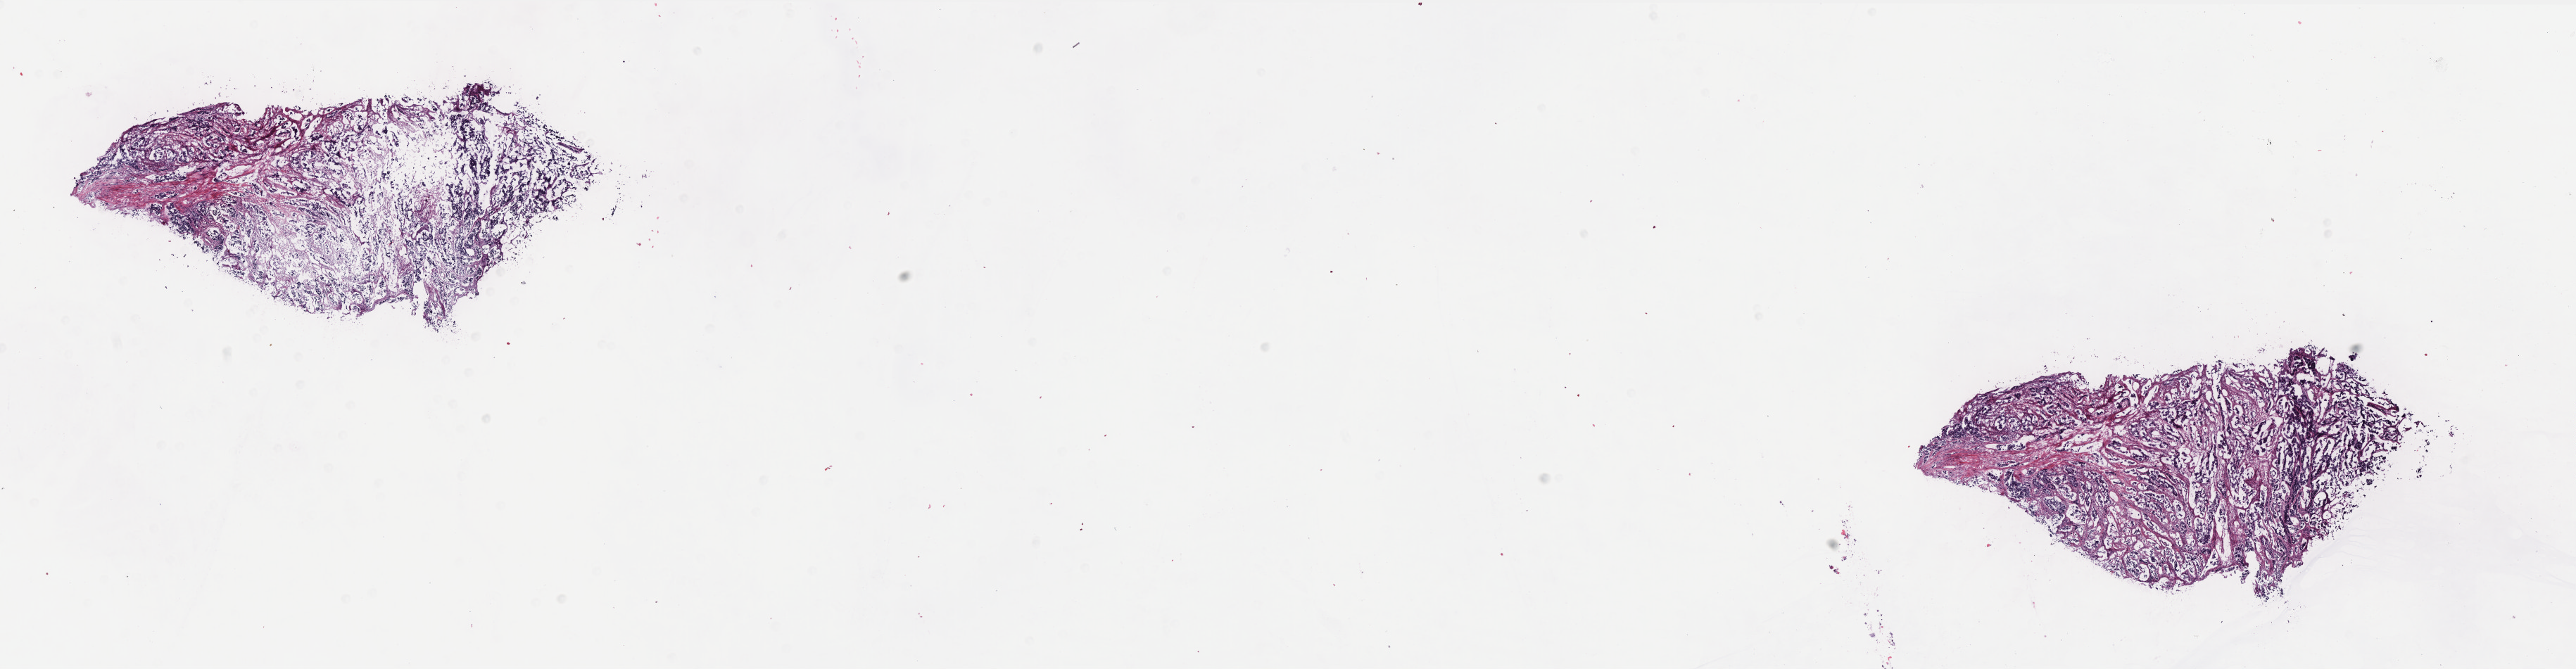
Hematoxylin and eosin (H&E) stained whole-slide image — a low-resolution overview of the entire scanned area, about 29.3 x 7.6 mm (slide scanned at 40x), frozen section, primary tumour sample from the uterus. Patient: female, age at initial diagnosis 70 years. Histologic grade: G3 (poorly differentiated). Pathologist review of this section (percent, as recorded): tumour cells 60%, tumour nuclei 70%, normal cells 30%, stromal cells 0%, necrosis 10%. Inflammatory infiltration, as recorded: lymphocyte infiltration 10%, monocyte infiltration 0%, neutrophil infiltration 10%.
Pathologic diagnosis: Serous cystadenocarcinoma, NOS. FIGO stage: IIIC2.